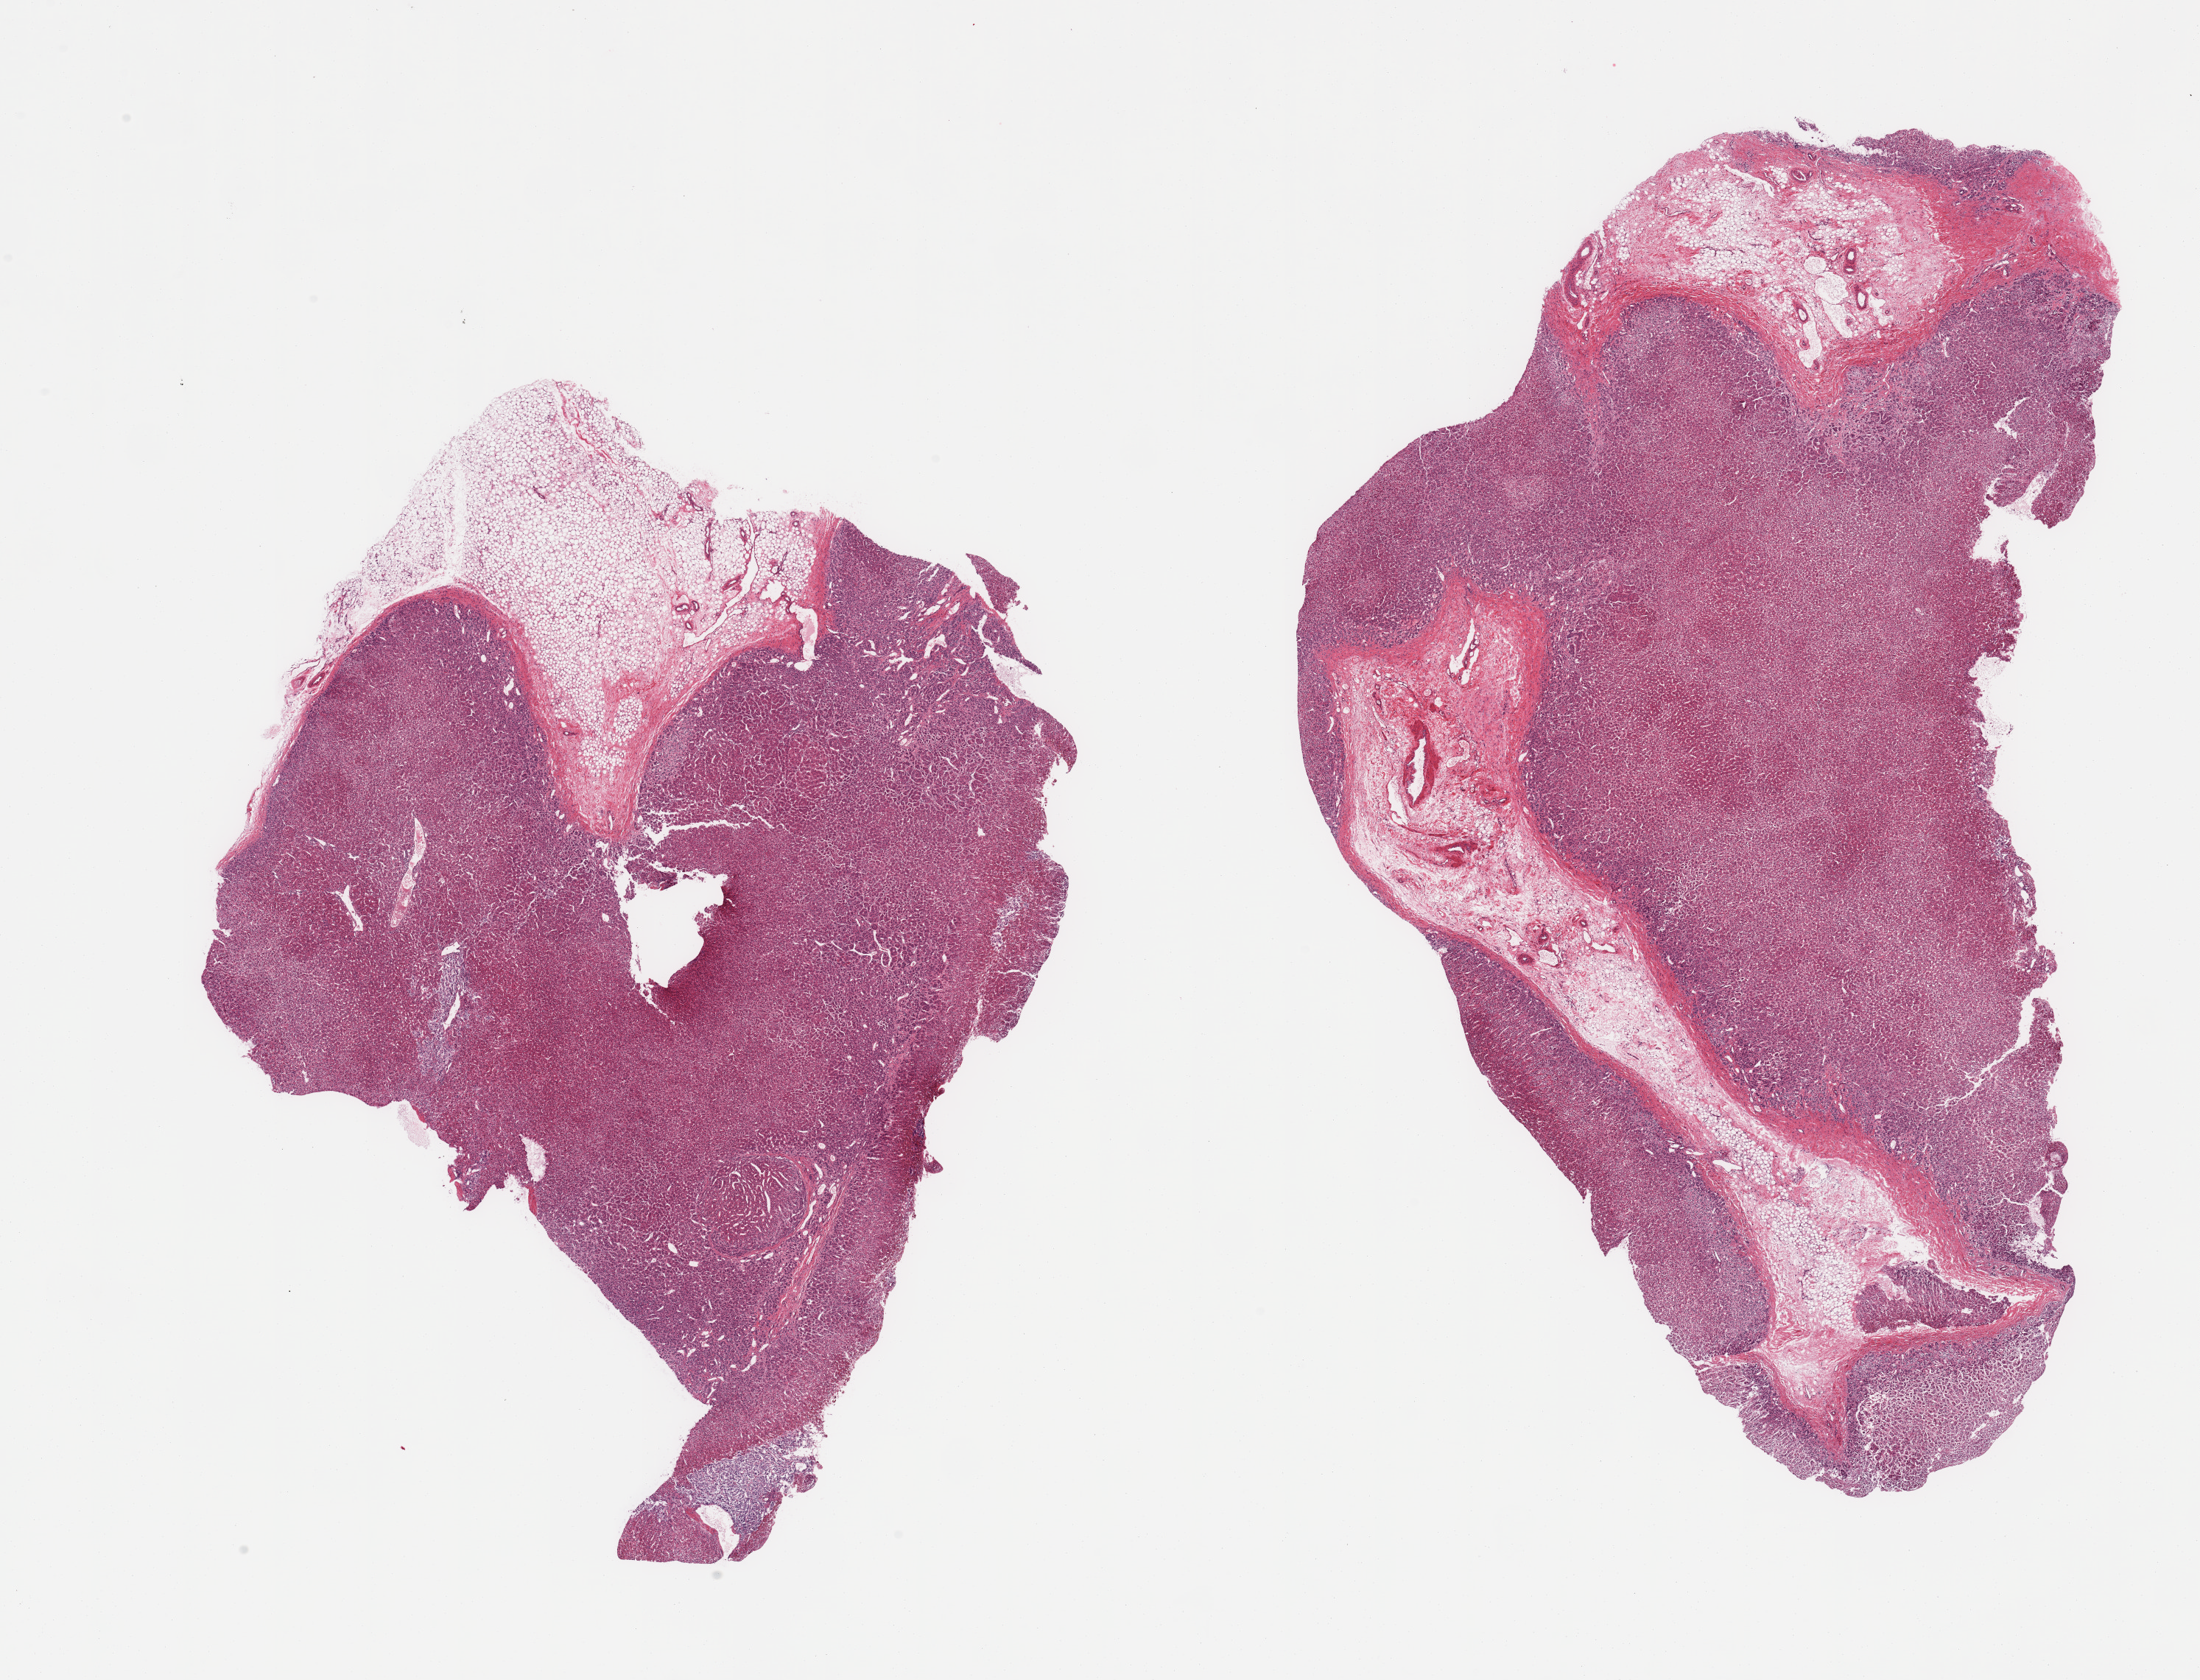
Hematoxylin and eosin (H&E) whole-slide image, a low-resolution overview of the entire scanned area, about 23.6 x 18.0 mm, PAXgene-fixed, paraffin-embedded tissue, sampled site (target tissue): adrenal gland, tissue donor sample. Donor sex: male.
Pathologist's review note for this sample: 2 pieces; 20% of each is fat/fibrovascular tissue, cortex and small portion of medulla.